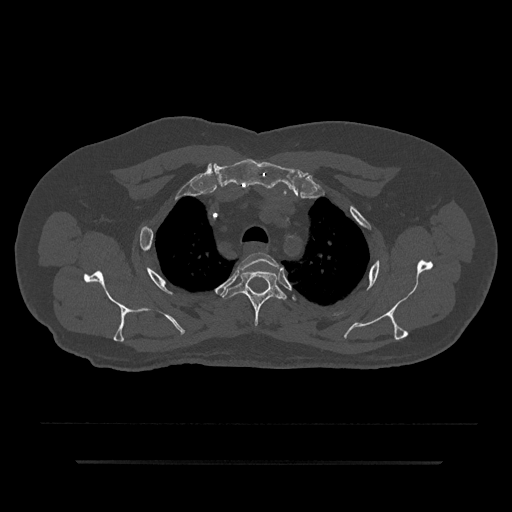
CT including the spine, one axial slice; slice 665 of 797 in the series (ordered by position); reconstruction kernel Br40s/3; bone window (W 1800 / L 400 HU); 0.5 mm slice thickness; 512 × 512 image matrix, field of view 464 × 464 mm. Male patient, age 59 years. From the clinical record (not read from this slice): primary cancer: bile ducts.
Annotated regions visible in this slice (semi-automatic segmentation, software-assisted and operator-edited):
- T2 vertebra: box from (x=237, y=252) to (x=281, y=272) px
- T3 vertebra: (x=223, y=269)–(x=287, y=327)